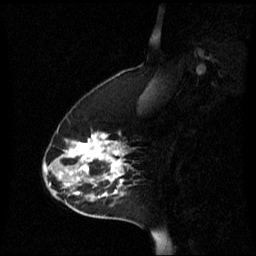
Breast MRI (dynamic contrast-enhanced), one sagittal slice. Slice 19 of 60 in the series (ordered by position). Dynamic contrast-enhanced series, image 2 of 3 at this slice position (ordered by acquisition). 1.5 T. TE 4.2 ms, TR 8.4 ms. 2.2 mm slice thickness. 256 × 256 image matrix, field of view 240 × 240 mm. Female patient, age 45 years. From the clinical record (not read from this slice): setting: breast cancer imaged before/during neoadjuvant chemotherapy; receptor status: HR-positive, HER2-negative.
Structures marked on this image (semi-automatic segmentation, software-assisted and operator-edited):
- analysis volume of interest (the breast-tissue region the enhancement analysis was run in; not a lesion): bounding box (x1, y1, x2, y2) in pixels: (42, 132, 135, 221)
- tumour enhancement mask (voxels above the 70 % enhancement threshold inside the analysis volume of interest): (44, 134, 125, 201)